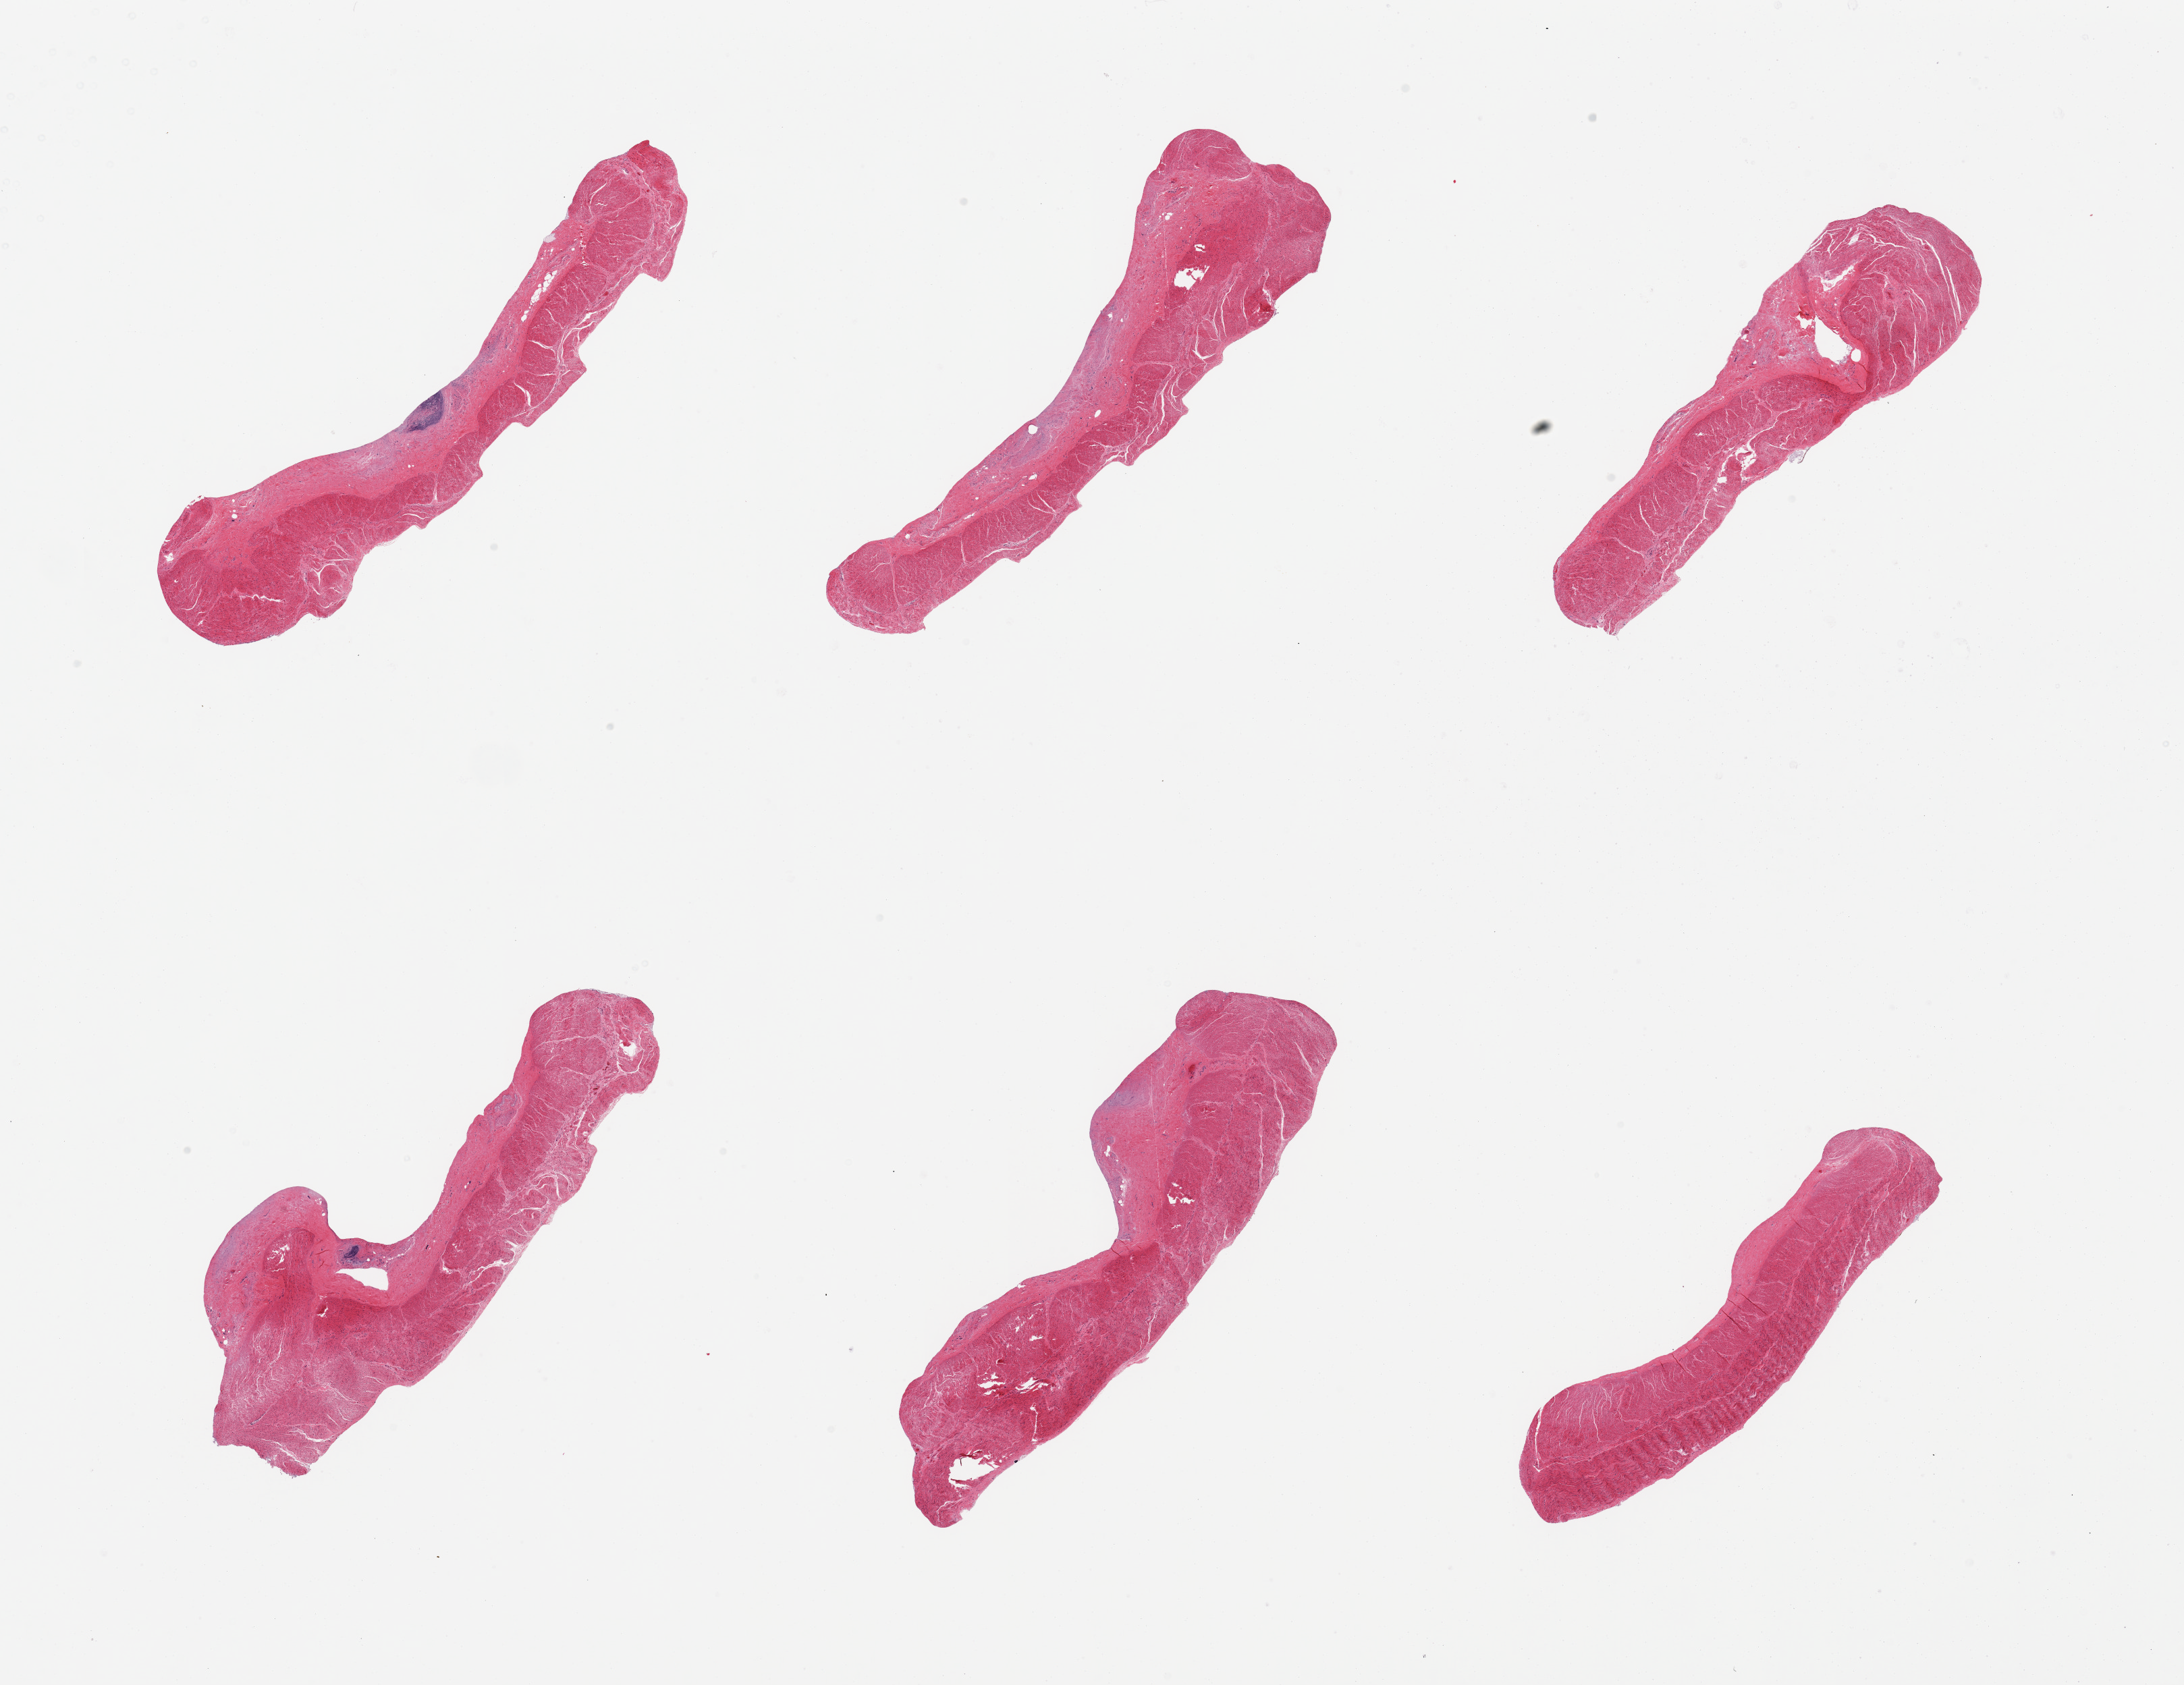
Hematoxylin and eosin (H&E) whole-slide image, shown as a low-resolution overview of the whole scanned area (about 25.6 x 19.7 mm), PAXgene-fixed paraffin-embedded (PFPE) section, sampled site (target tissue): sigmoid colon, tissue donor sample. Donor sex: male.
Review note (as recorded): 6 pieces; 40% fibrous content.